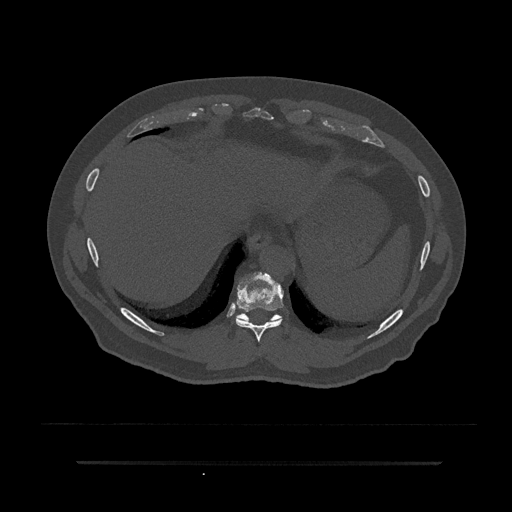
CT including the spine, one axial slice. Slice 361 of 797 in the series (ordered by position). Reconstruction kernel Br40s/3. 120 kVp. Bone window (W 1800 / L 400 HU). 0.5 mm slice thickness. 512 × 512 image matrix, field of view 464 × 464 mm. Male patient, age 59 years. From the clinical record (not read from this slice): primary cancer: bile ducts.
Outlined on this slice (semi-automatic segmentation, software-assisted and operator-edited):
- T10 vertebra: bounding box [x1, y1, x2, y2] px = [237, 313, 280, 325]
- T9 vertebra: [236, 272, 284, 342]